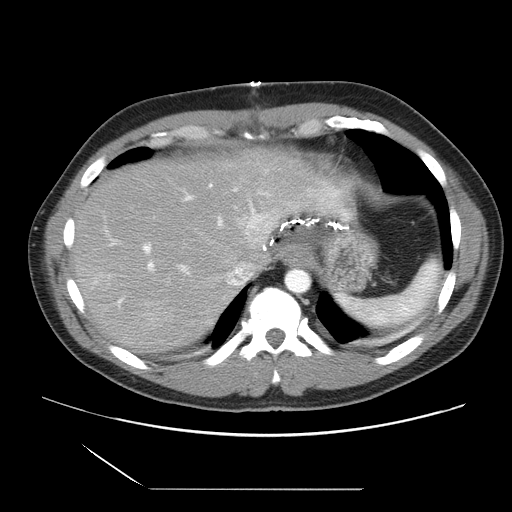
Contrast-enhanced abdominal CT, one axial slice. Position 25 of 39 along the scan axis. 120 kVp. Intravenous contrast given. Soft-tissue window (W 400 / L 40 HU). 5 mm slice thickness. 512 × 512 image matrix, field of view 395 × 395 mm. Male patient, age 39 years. From the clinical record (not read from this slice): diagnosis: colorectal cancer liver metastases, imaged before liver resection; multiple liver metastases: yes; largest metastasis: 1.3 cm; disease in both lobes: no.
Structures marked on this image (manually delineated by an expert):
- hepatic veins: bounding box <168,237,252,308> (left, top, right, bottom; pixels)
- liver: <72,149,351,354>
- planned liver remnant (the part of the liver to remain after resection): <120,149,351,265>
- portal vein (with intrahepatic branches): <104,193,257,308>